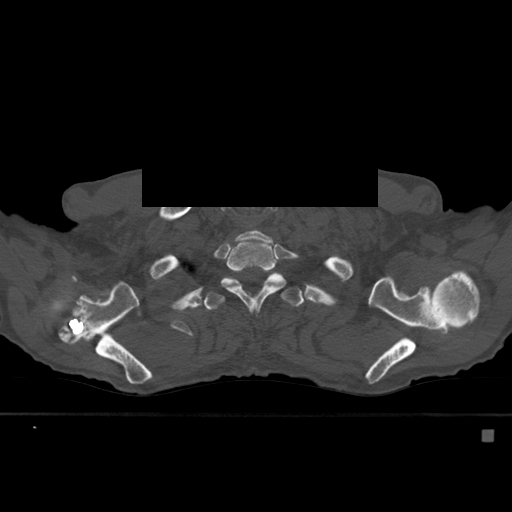
CT including the spine, one axial slice. Position 443 of 527 along the scan axis. Bone window (W 1800 / L 400 HU). 1.5 mm slice thickness. 512 × 512 image matrix, field of view 373 × 373 mm. Patient: male, 78 years. Case-level facts recorded for this patient, not image findings: primary cancer: prostate.
Structures marked on this image (semi-automatically segmented with operator editing):
- T1 vertebra: bounding box <246,230,273,242> (left, top, right, bottom; pixels)
- T2 vertebra: <223,230,284,311>
- T3 vertebra: <204,273,302,311>